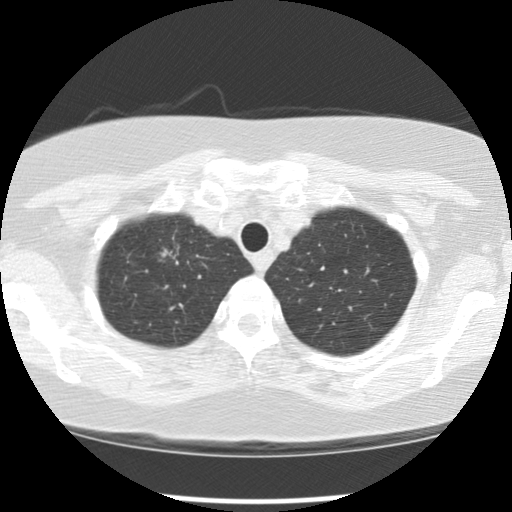
Low-dose screening chest CT, one axial slice. Position 98 of 113 along the scan axis. Reconstruction kernel STANDARD. Lung window (W 1500 / L -600 HU). 512 × 512 image matrix, field of view 318 × 318 mm.
Annotated regions visible in this slice (outlined manually by an expert reader):
- lesion 1 (tumor, upper lobe of right lung): bounding box <160,249,176,259> (left, top, right, bottom; pixels)